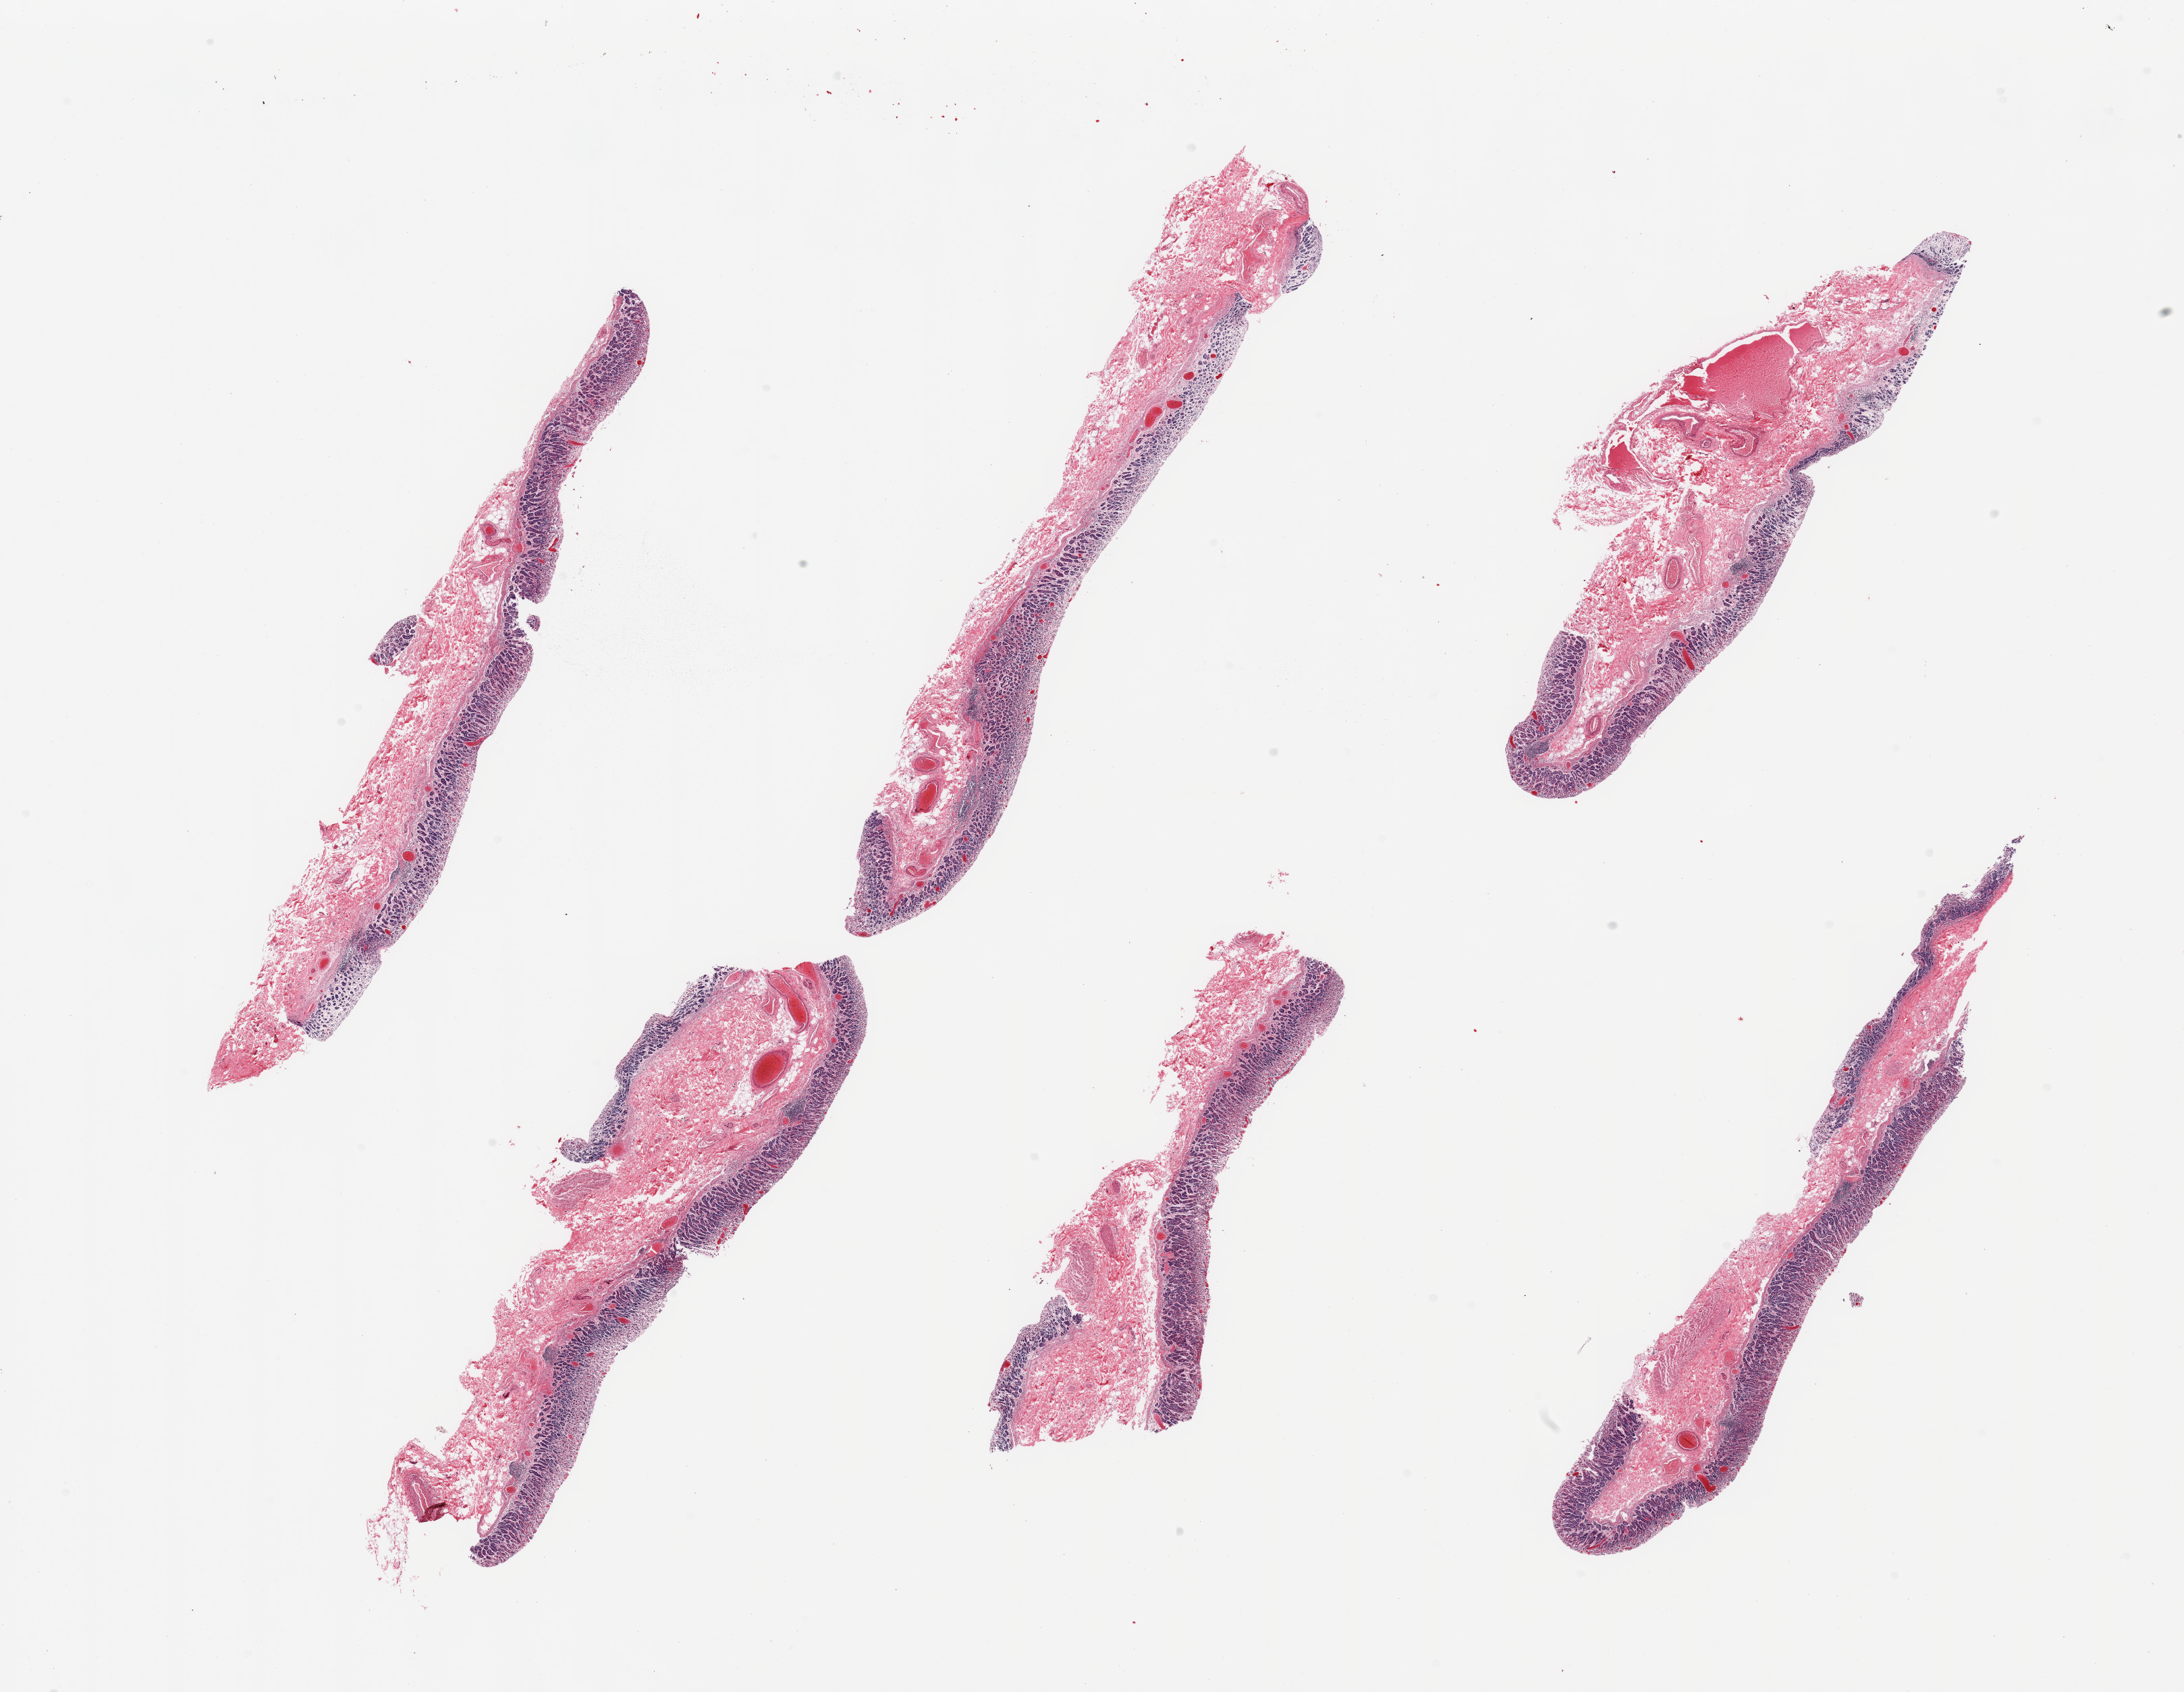
Hematoxylin and eosin (H&E) whole-slide image — low-resolution overview of the scanned area, about 25.6 x 19.8 mm. PAXgene-fixed paraffin-embedded (PFPE) section. Section of stomach (target tissue). Tissue donor sample. Male donor.
* pathologist's review note for this sample: 6 pieces; predominantly moderately autolyzed gastric mucosa with small foci of muscularis in 3 of 6 pieces; congestion